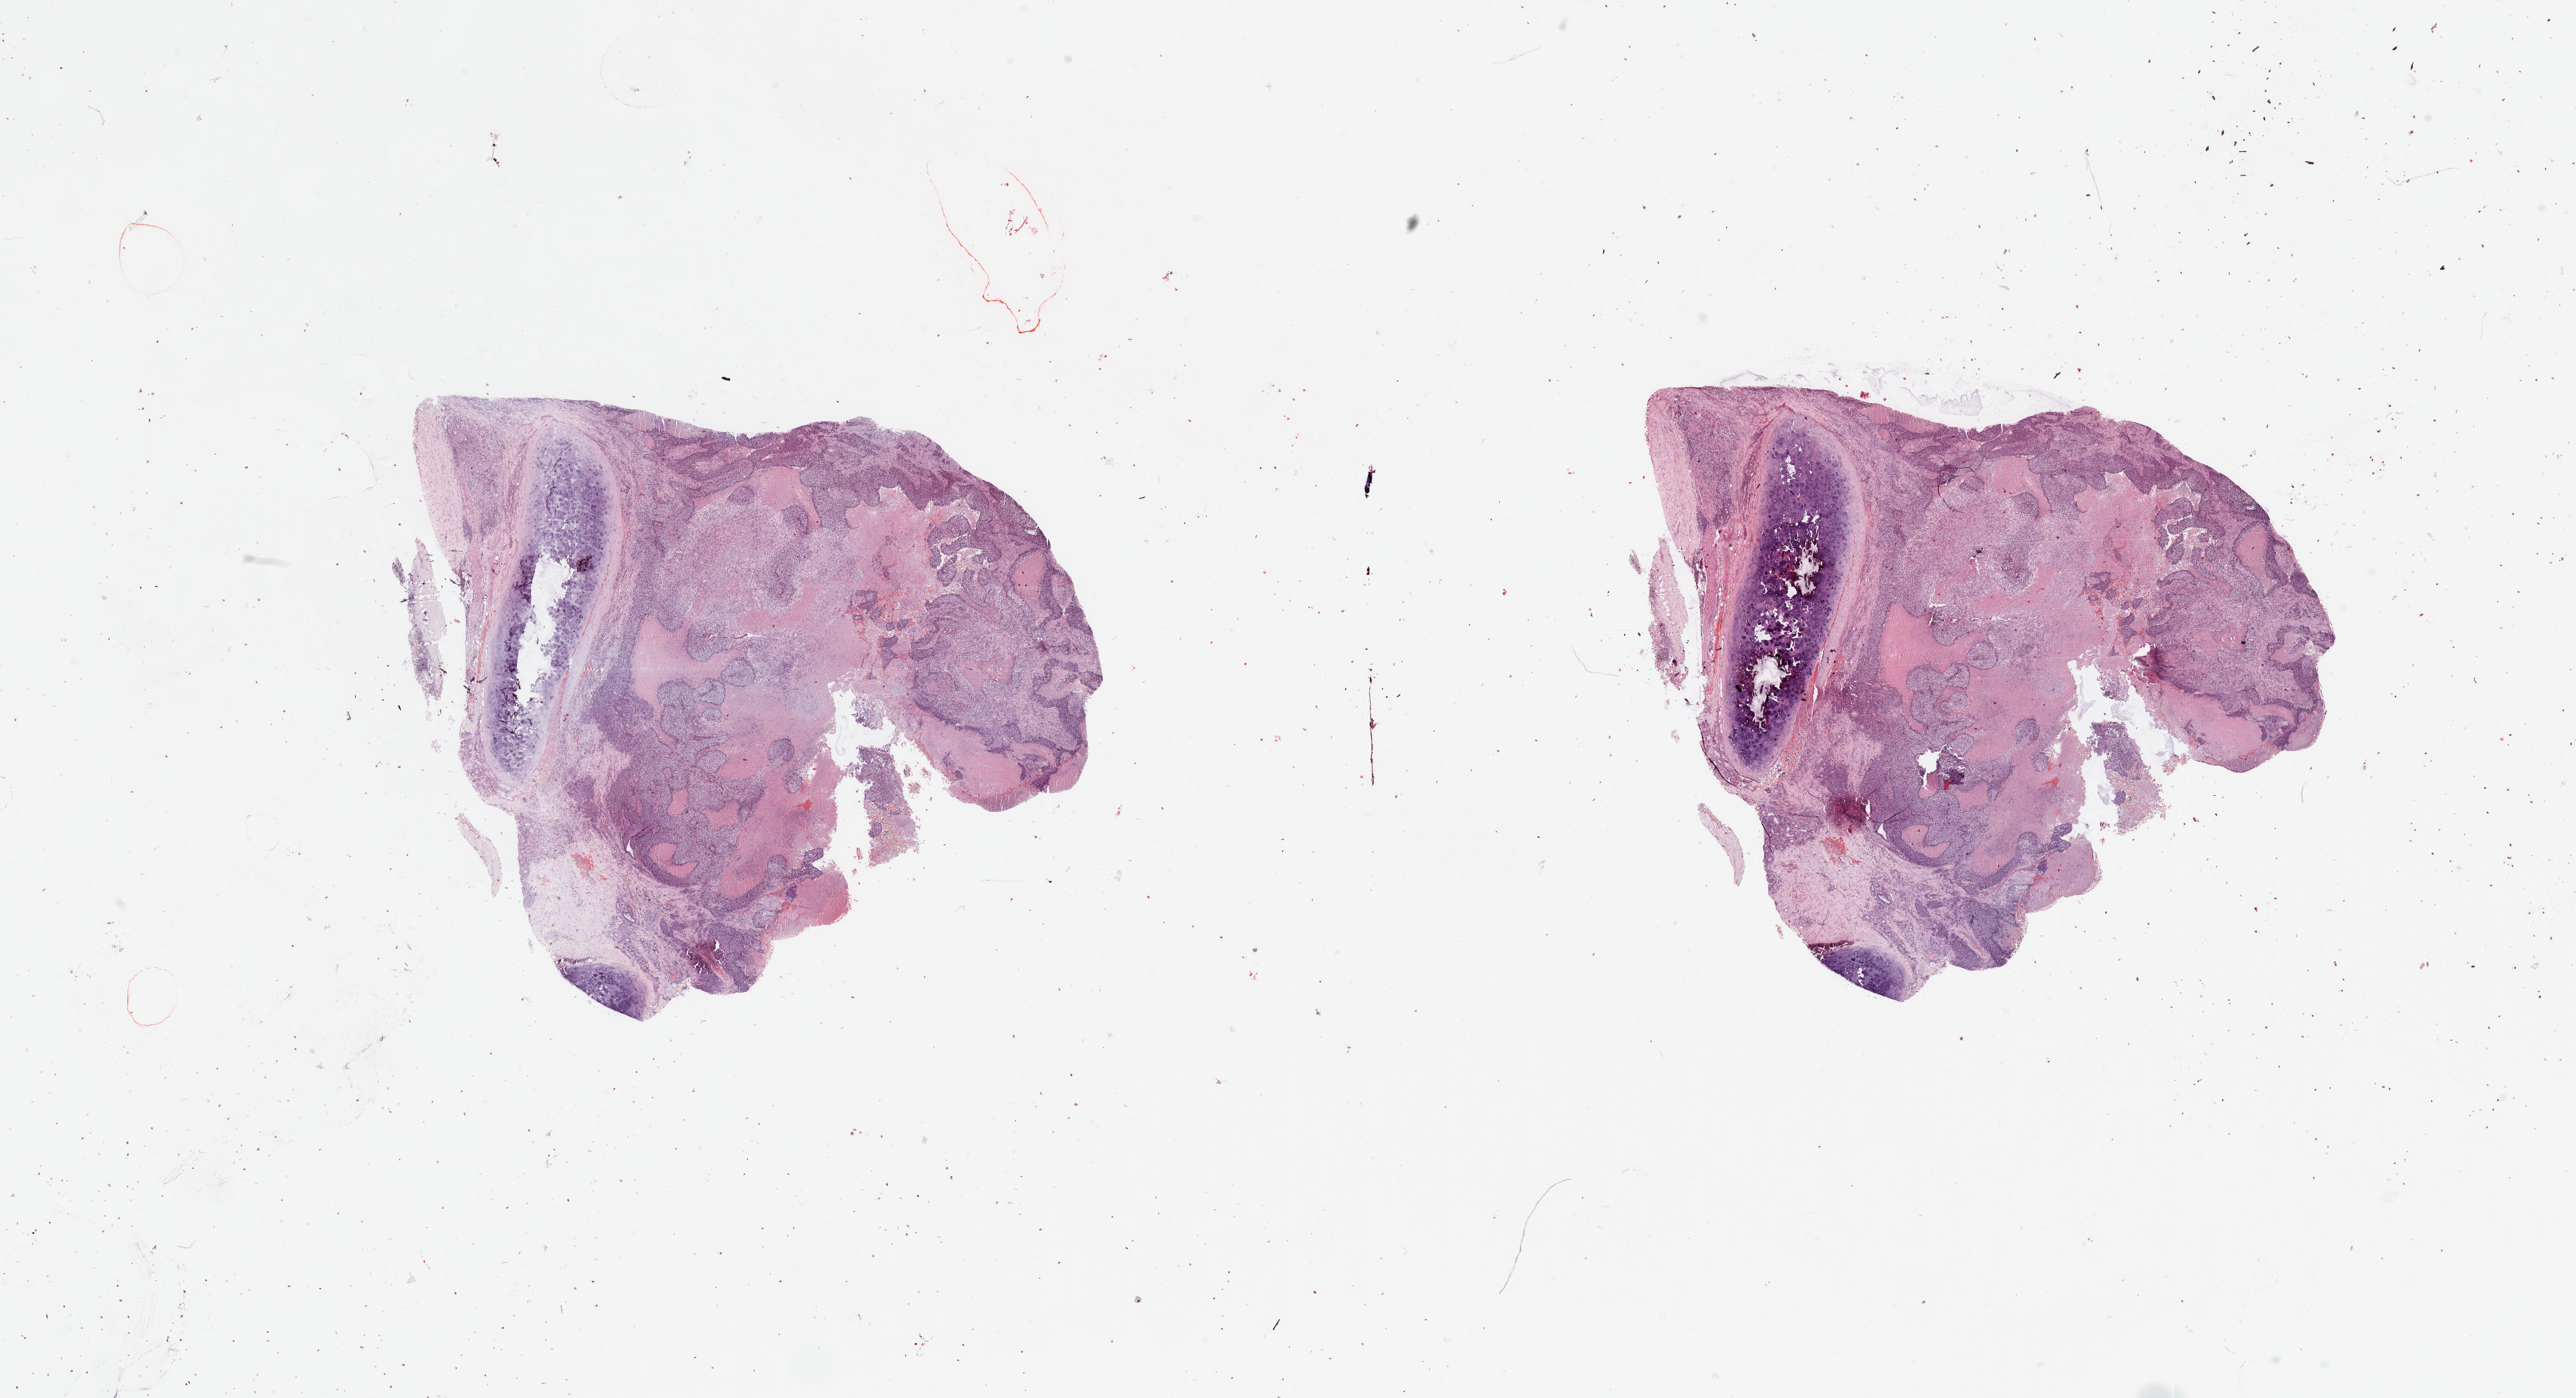
Whole-slide histology image, H&E, shown as a low-resolution overview of the whole scanned area (about 31.5 x 17.1 mm, acquisition: 20x scan), lung, tumour tissue. Patient: male, age 65 years. Histologic grade: G3 (poorly differentiated).
AJCC pathologic stage: IB. Histologic diagnosis: Squamous cell carcinoma, NOS.